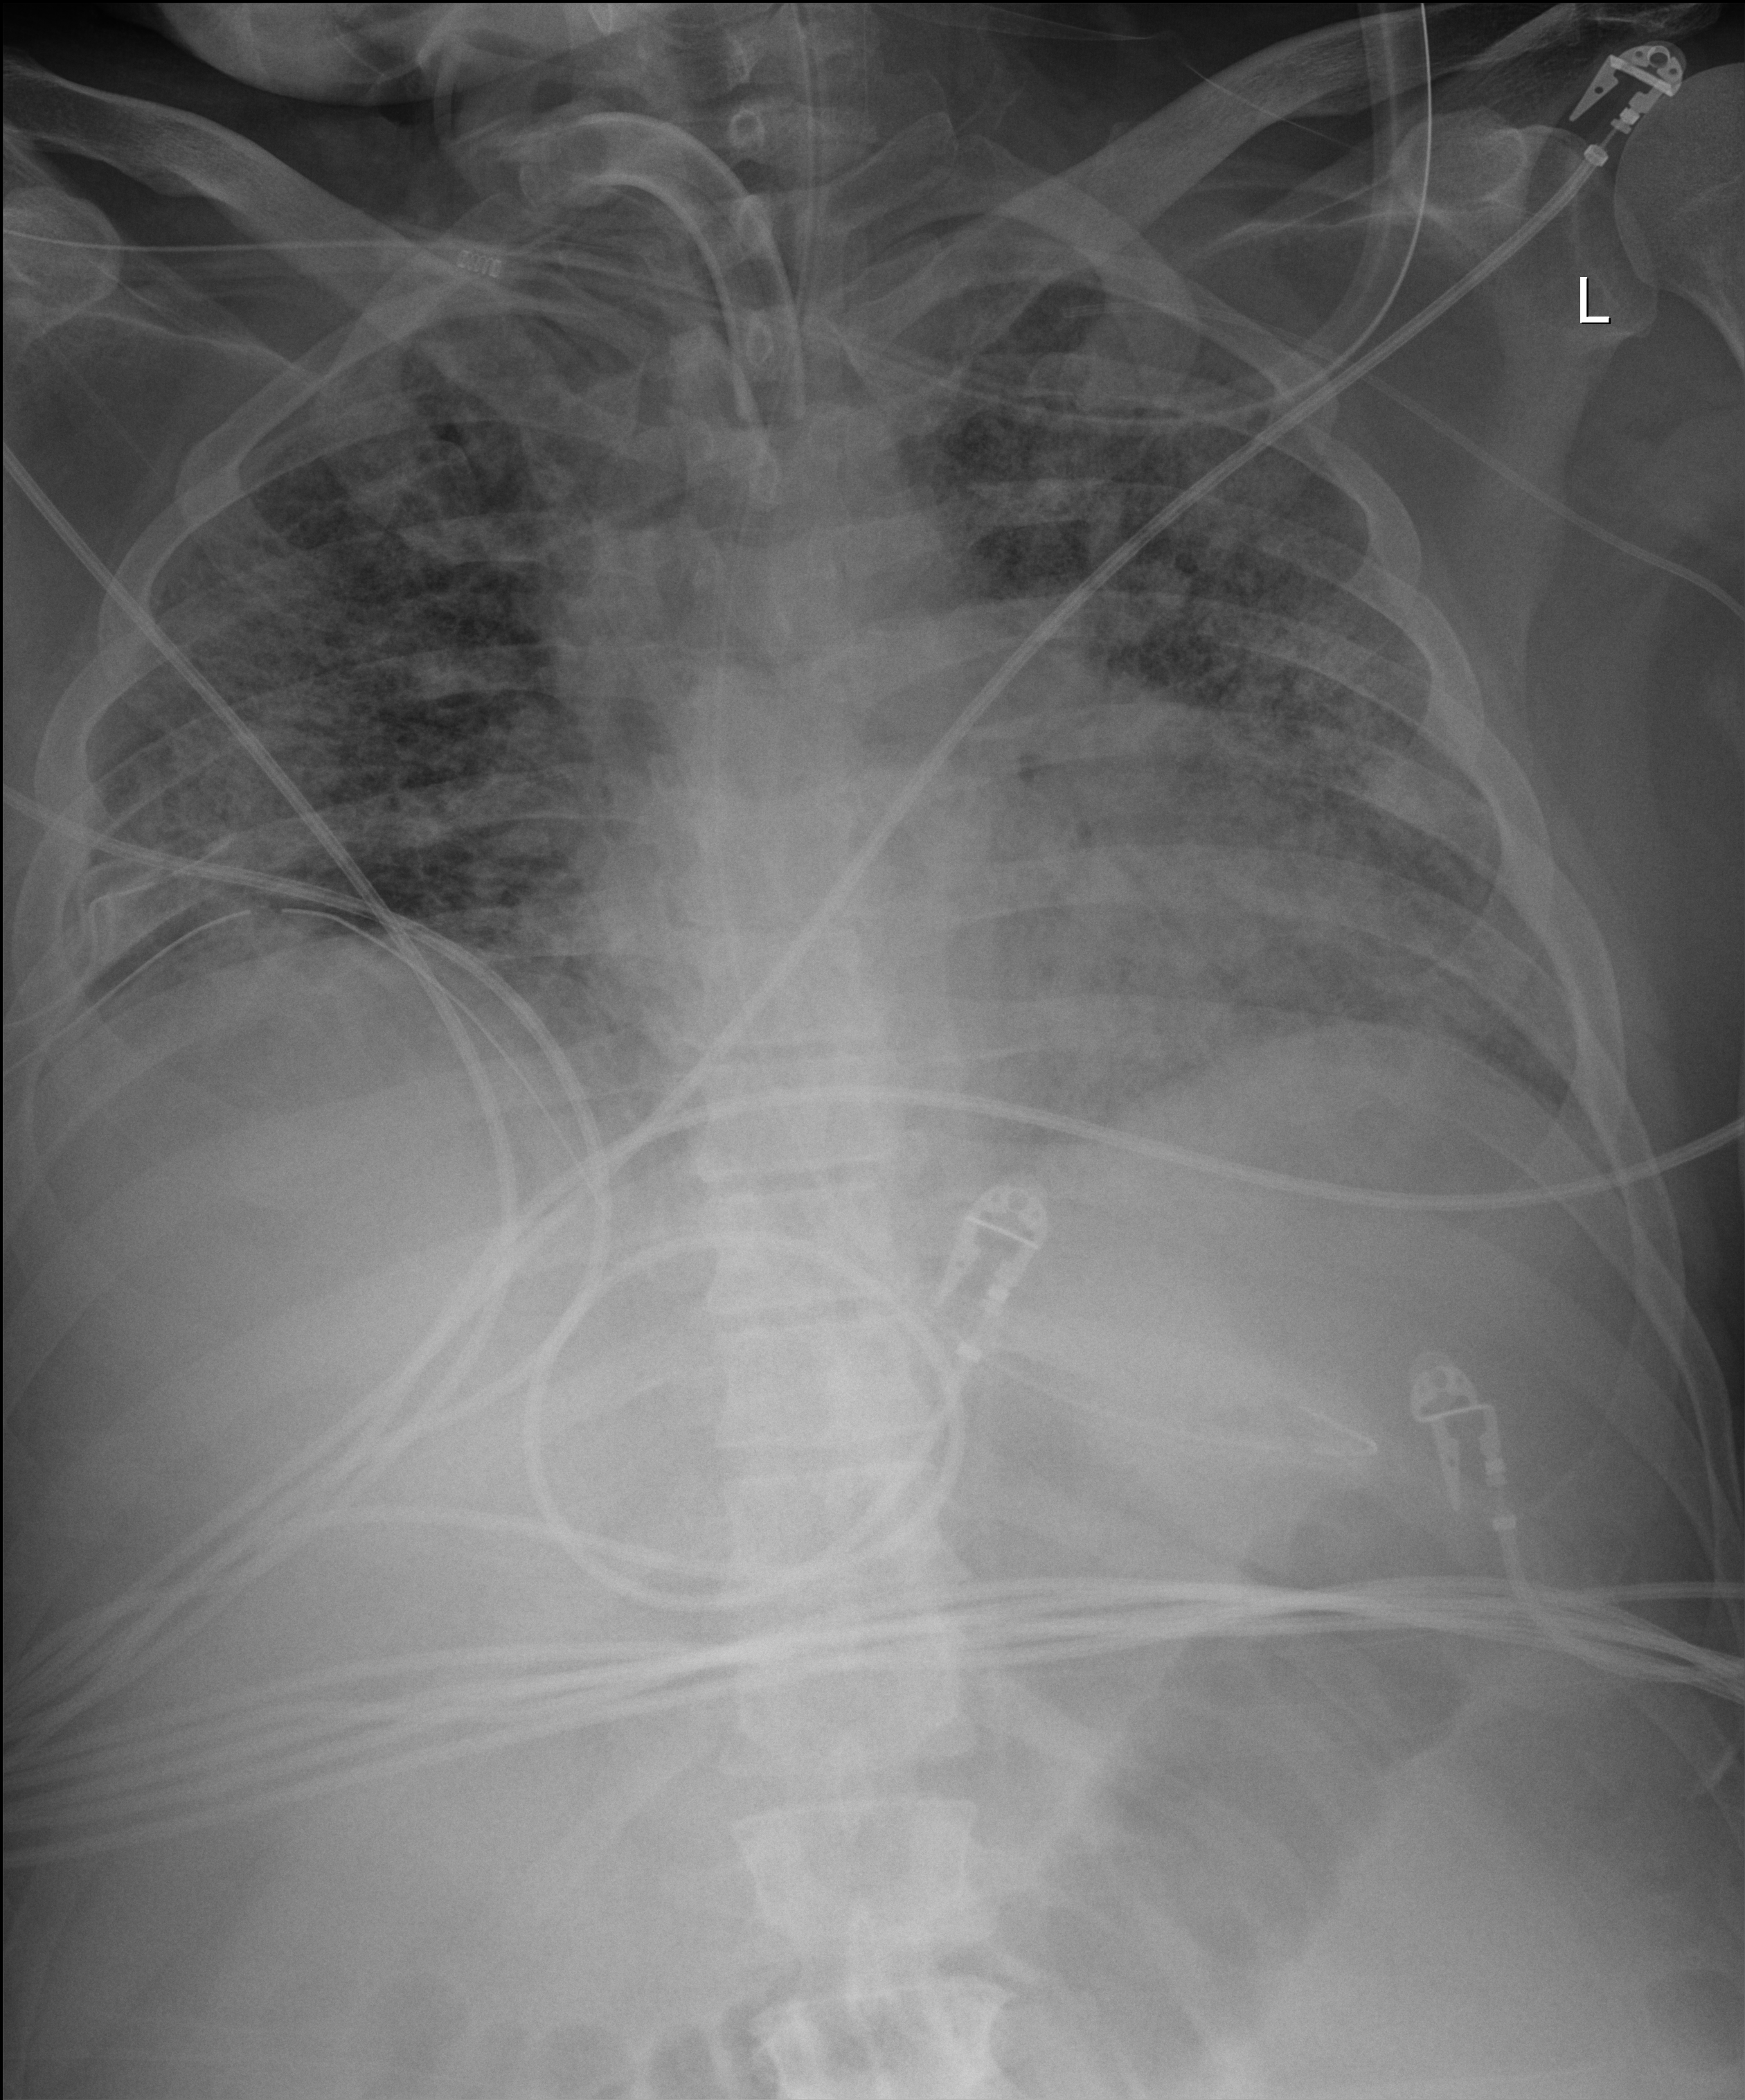
Chest X-ray (portable), anteroposterior (AP) projection. Patient hospitalised with COVID-19; male, aged 18–59 years.
Hospital-stay facts (about this admission, not read from this image; timing relative to this image not recorded): admitted to intensive care during this hospital stay: yes.